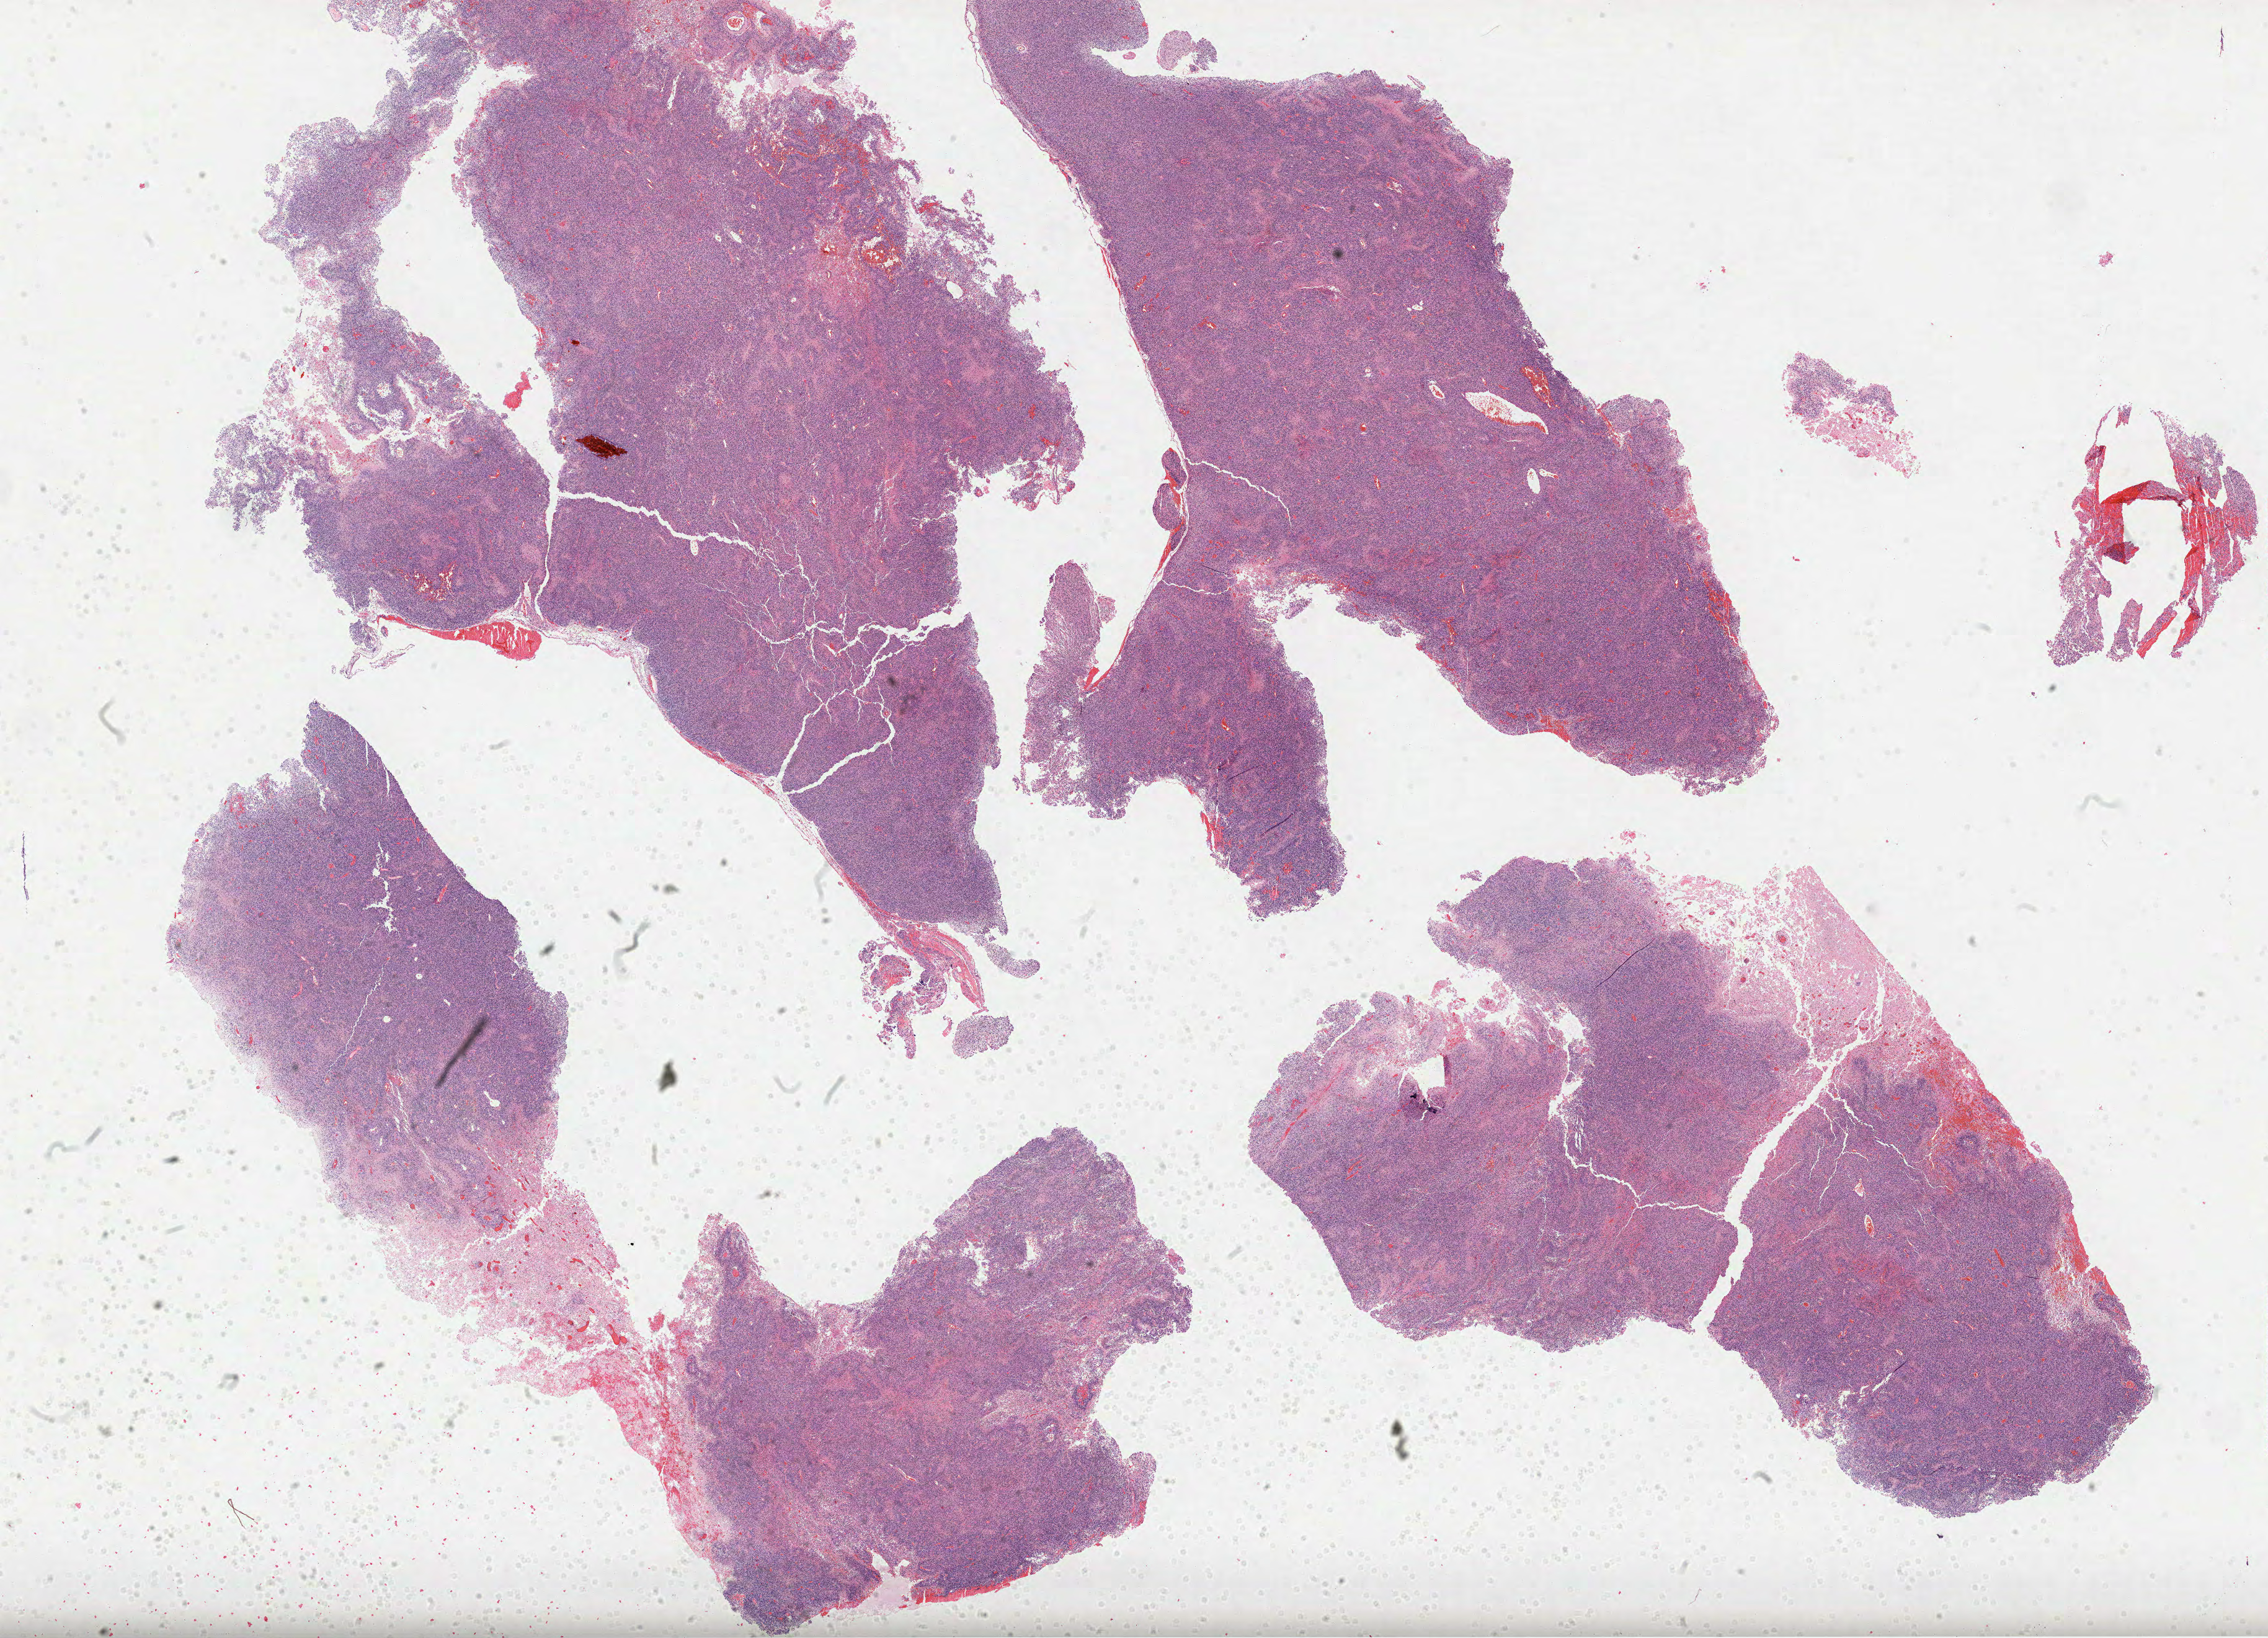
H&E whole-slide image — whole scanned area (about 29.5 x 21.3 mm) shown as a low-resolution overview. Formalin-fixed paraffin-embedded (FFPE) diagnostic section. Primary tumour sample from the brain. Male, age 64 years at initial diagnosis.
Pathologic diagnosis: Glioblastoma.